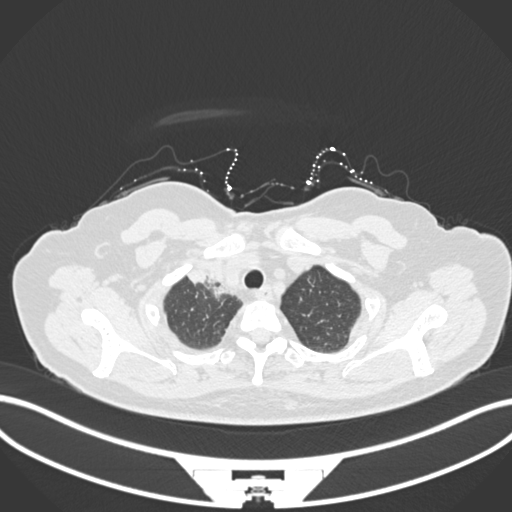
Chest CT, one axial slice. Slice 149 of 172 in the series (ordered by position). Reconstruction kernel B30f. Lung window (W 1500 / L -600 HU). 512 × 512 image matrix. Patient: female, 52 years. Case-level facts recorded for this patient, not image findings: clinical TNM (as recorded): T3 N1 M1.
Structures marked on this image (rectangle marked by the reading radiologist):
- lung tumour (recorded histology: adenocarcinoma): bounding box (x1, y1, x2, y2) in pixels: (187, 264, 231, 303)